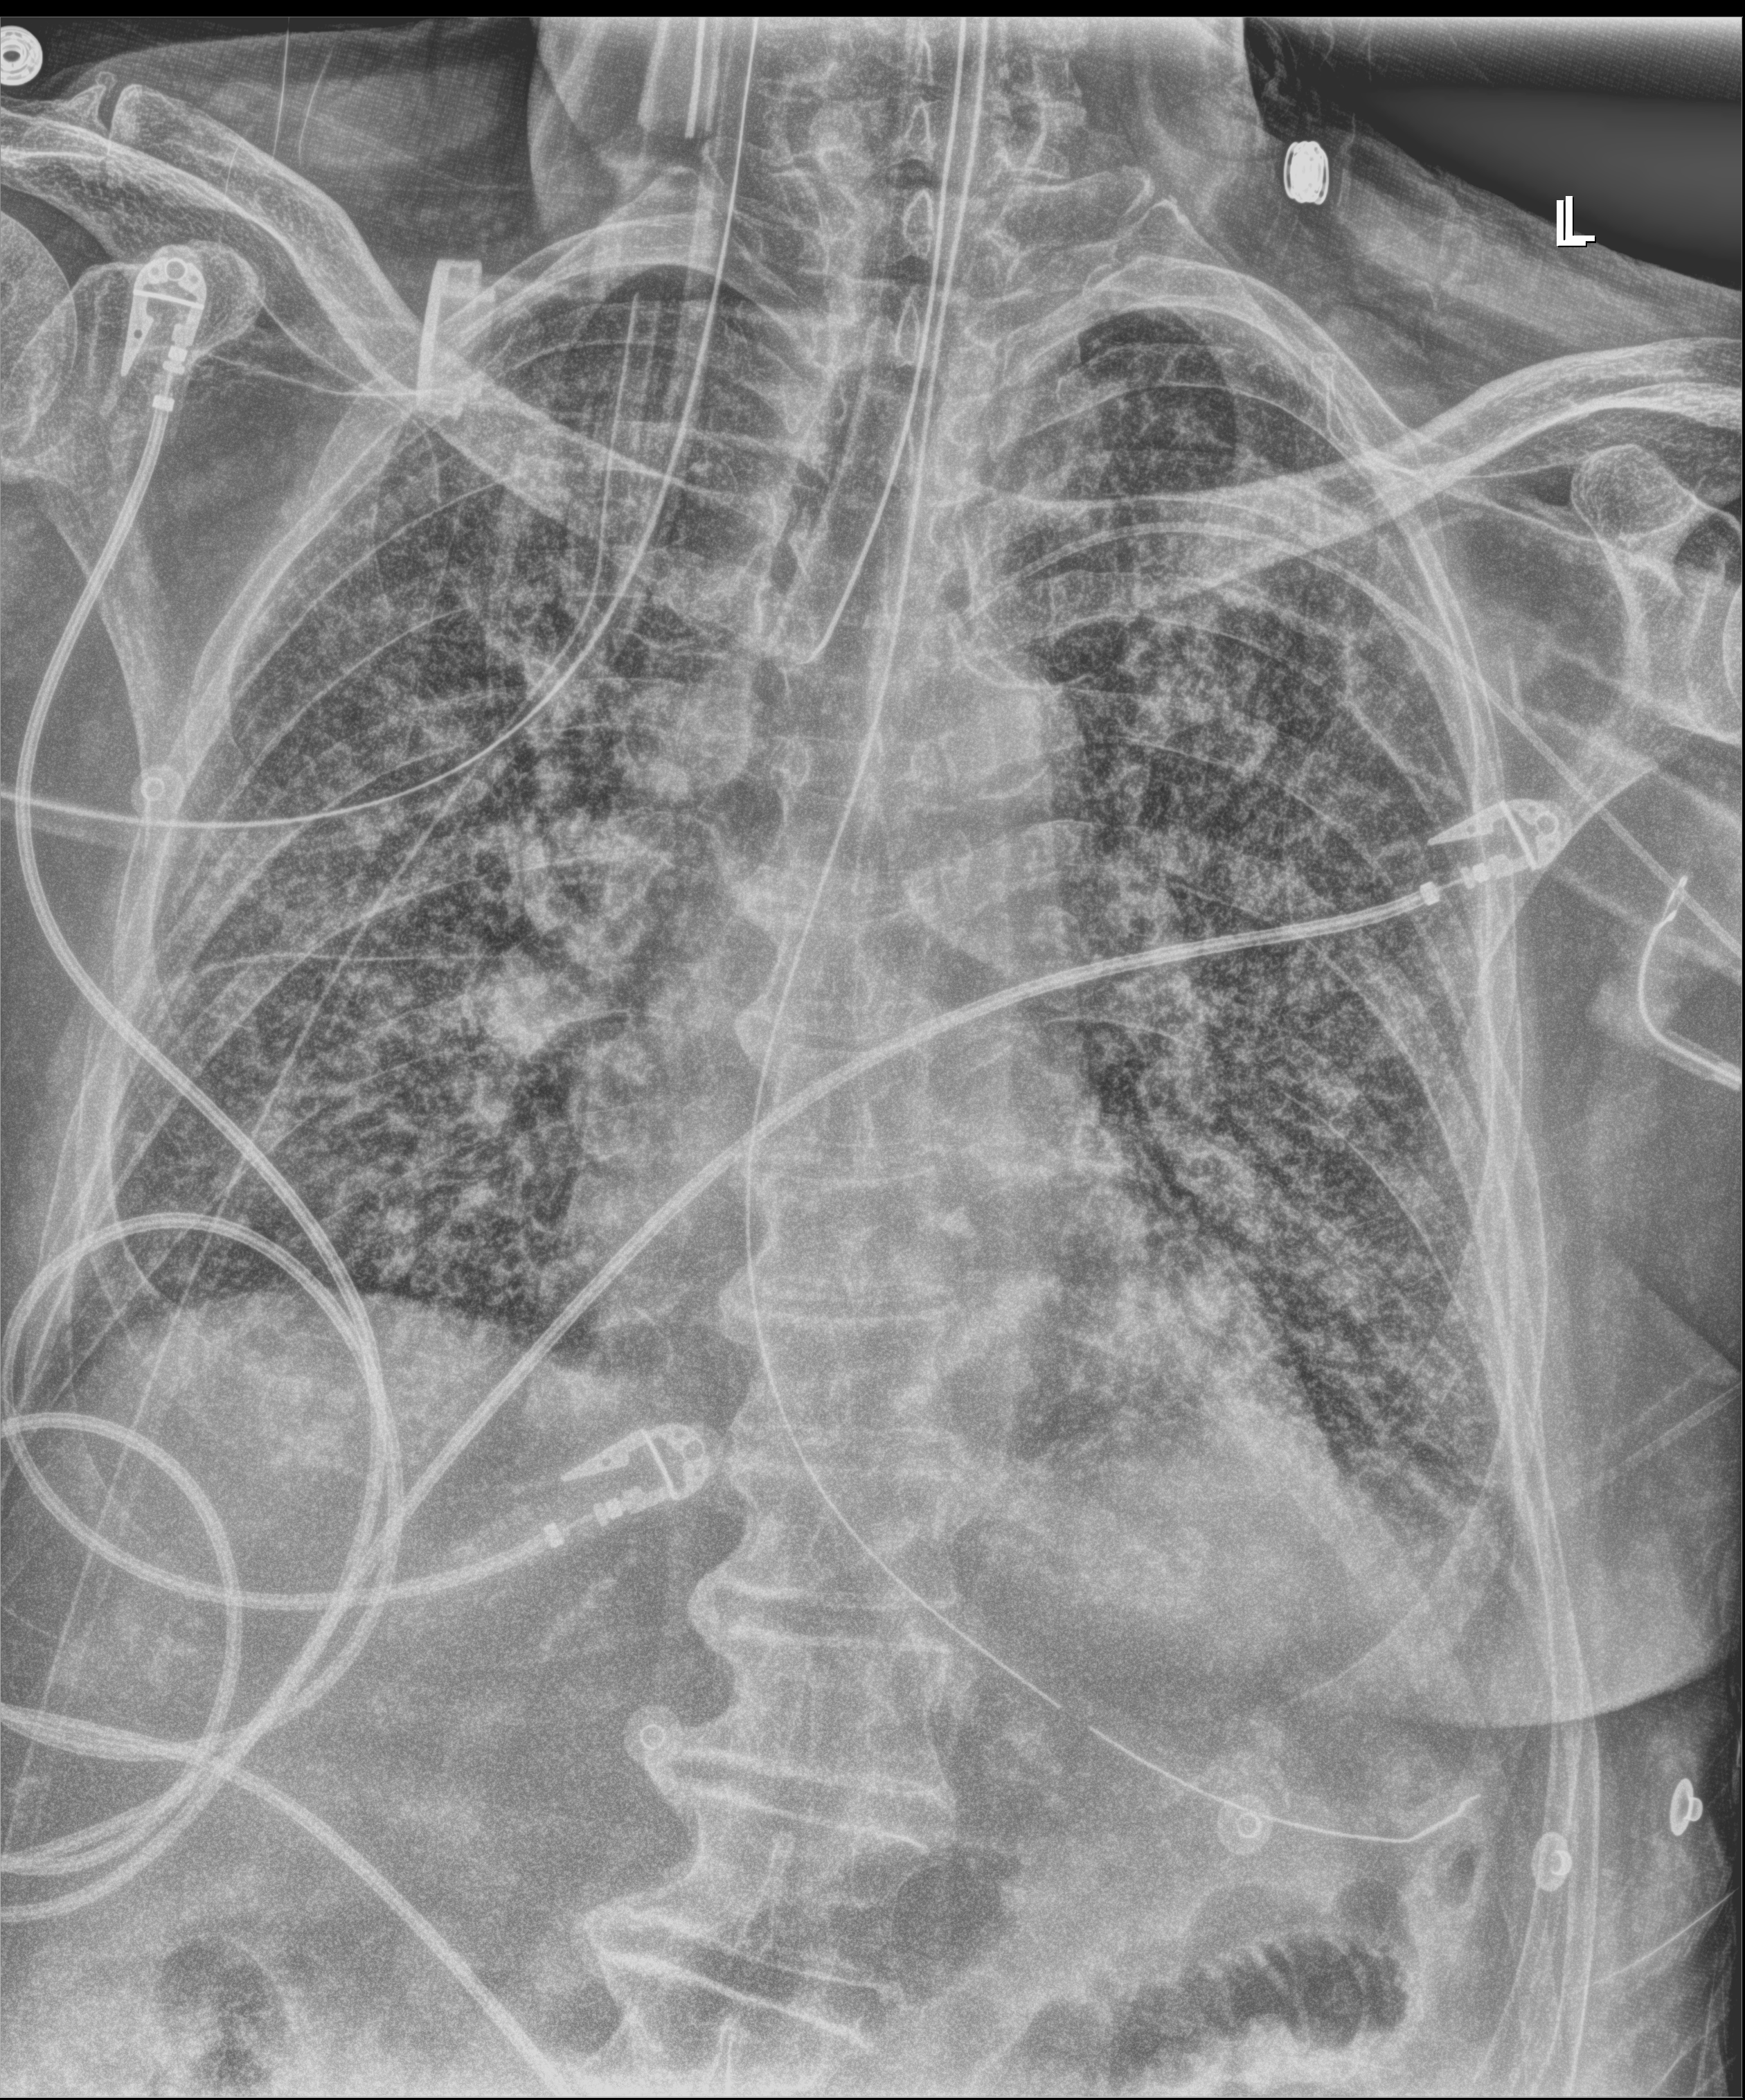
Chest radiograph; anteroposterior (AP) projection. Patient hospitalised with COVID-19; male, aged 75–90 years.
Hospital-stay facts (about this admission, not read from this image; timing relative to this image not recorded): diabetes (admission record): no.